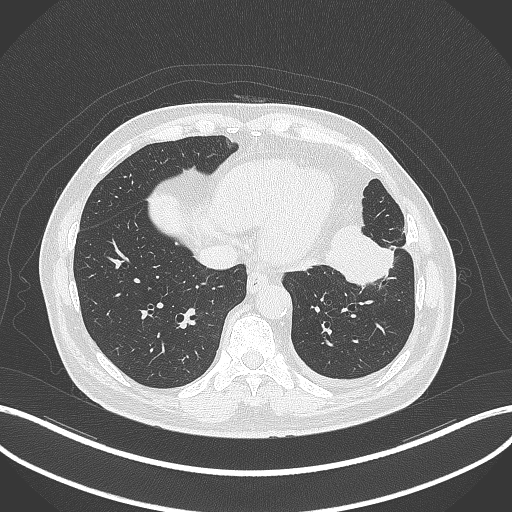
Chest CT, one axial slice. Position 102 of 230 along the scan axis. Reconstruction kernel B70f. Lung window (W 1500 / L -600 HU). 1 mm slice thickness. 512 × 512 image matrix, field of view 400 × 400 mm. Patient: male, 68 years. From the clinical record (not read from this slice): clinical TNM (as recorded): T2b N0 M0.
Outlined on this slice (rectangle marked by the reading radiologist):
- lung tumour (recorded histology: squamous cell carcinoma): bounding box [x1, y1, x2, y2] px = [319, 220, 398, 289]